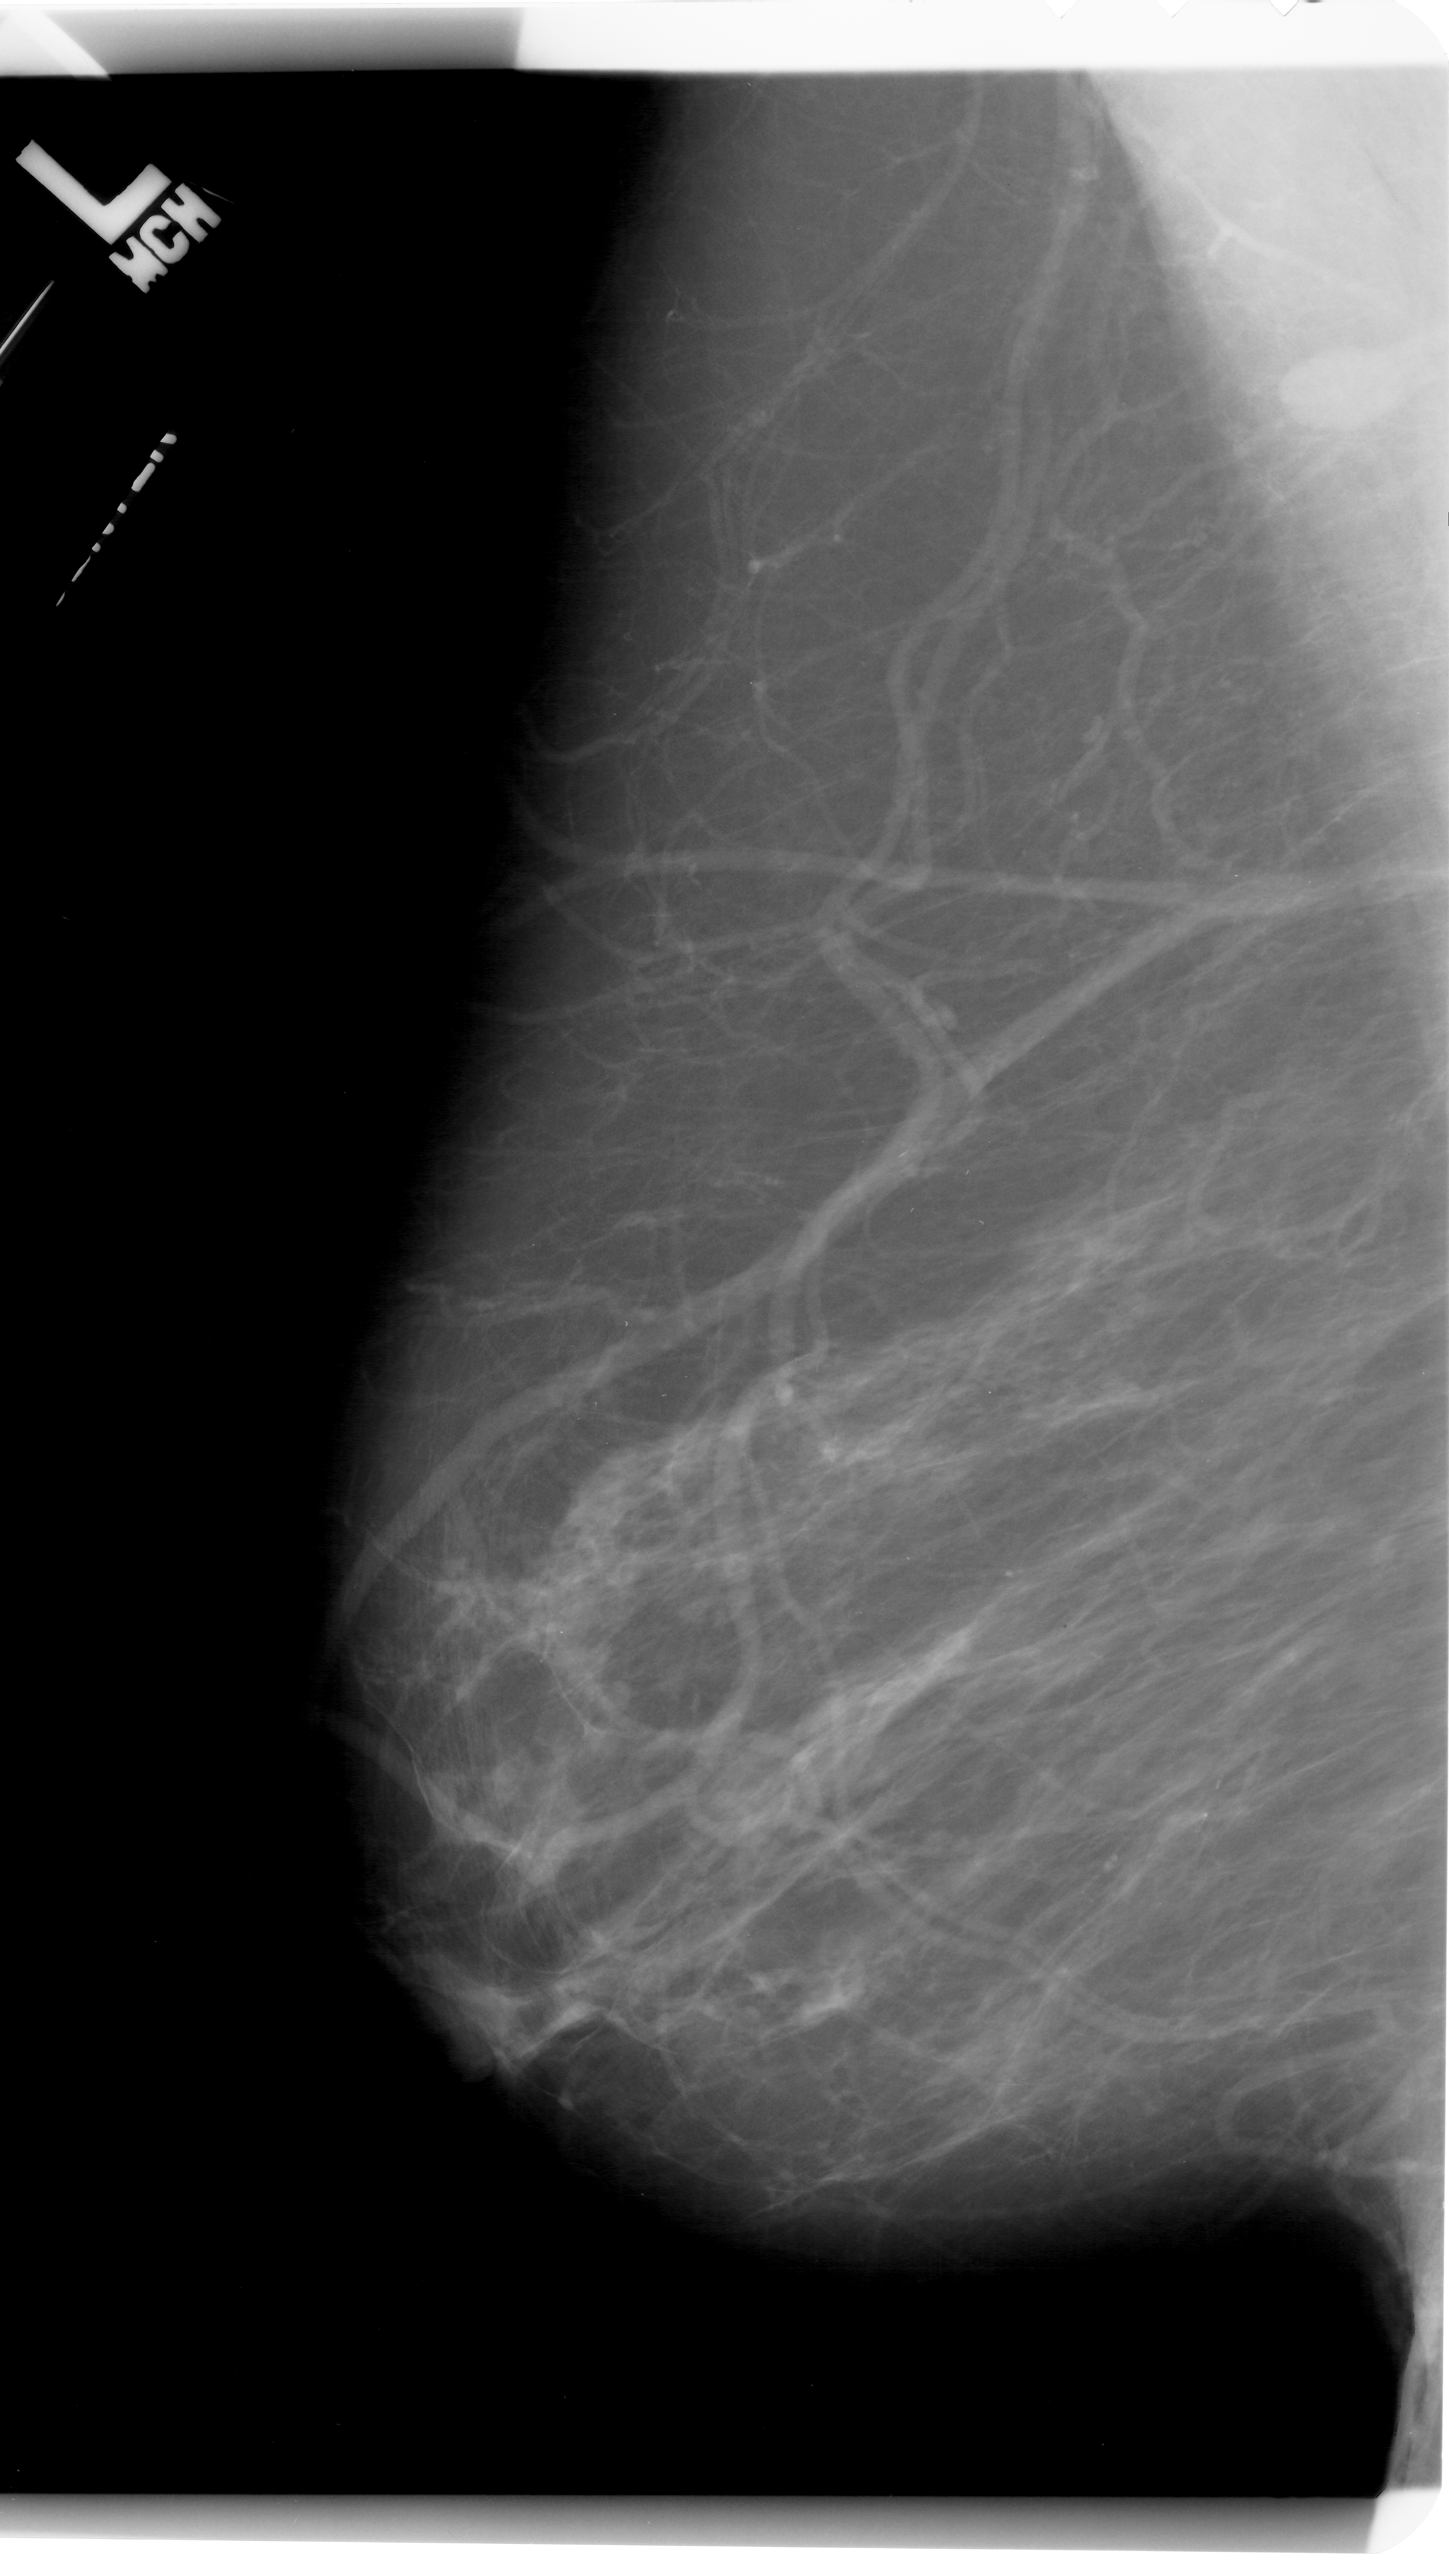
Mammogram (digitized film), left breast, MLO view, breast composition: scattered fibroglandular densities (BI-RADS density category 2 of 4).
- Calcifications, morphology fine linear branching, distribution linear; BI-RADS assessment category 4; pathology result (as recorded, not read from the image): malignant.